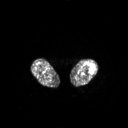
FDG PET of an extremity soft-tissue mass (from a PET/CT study), one axial slice. 3.27 mm slice thickness. 128 × 128 image matrix. Female patient, age 62 years. From the clinical record (not read from this slice): histological type: undifferentiated – high grade; grade: high; site of the primary tumour: left thigh.
Annotated regions visible in this slice (expert contour drawn on MRI and transferred to this co-registered scan by the dataset authors):
- gross tumour volume including surrounding oedema: box from (x=87, y=63) to (x=94, y=71) px